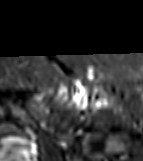
MRI of an extremity soft-tissue mass, one axial slice. Position 58 of 81 along the scan axis. STIR. MR volume resampled by the dataset authors to the PET/CT grid (not the native acquisition matrix). 3.27 mm slice thickness. 143 × 161 image matrix, field of view 140 × 157 mm. Female patient. Case-level facts recorded for this patient, not image findings: histological type: myxofibrosarcoma; grade: intermediate; site of the primary tumour: left thigh.
Outlined on this slice (expert contour drawn on MRI and transferred to this co-registered scan by the dataset authors):
- gross tumour volume including surrounding oedema: bounding box [x1, y1, x2, y2] px = [47, 83, 112, 105]